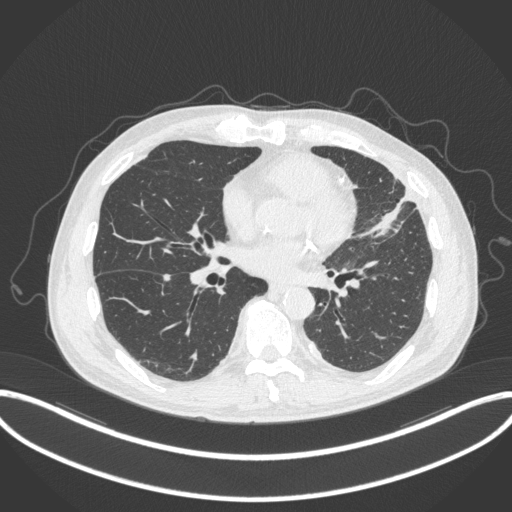
Chest CT, one axial slice. Slice 147 of 382 in the series (ordered by position). Reconstruction kernel B31f. 120 kVp. Lung window (W 1500 / L -600 HU). 1 mm slice thickness. 512 × 512 image matrix. Male patient, age 64 years. Case-level facts recorded for this patient, not image findings: clinical TNM (as recorded): T4 N1 M0; histopathological grade: G3.
Annotated regions visible in this slice (bounding box drawn by a radiologist):
- lung tumour (recorded histology: adenocarcinoma): box from (x=360, y=186) to (x=416, y=242) px